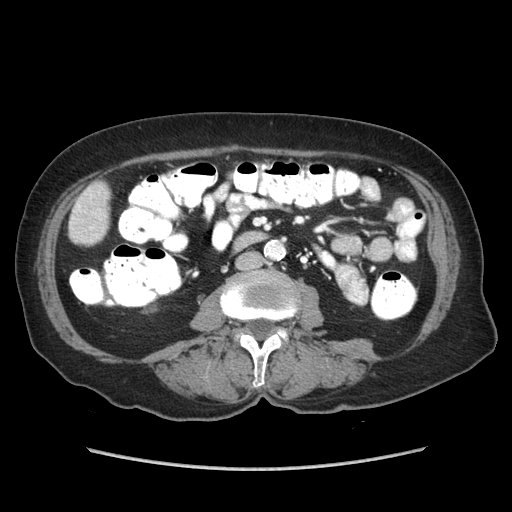
Contrast-enhanced abdominal CT (liver protocol), one axial slice; reconstruction kernel STANDARD; soft-tissue window (W 400 / L 40 HU); 2.5 mm slice thickness; 512 × 512 image matrix, field of view 360 × 360 mm. From the clinical record (not read from this slice): diagnosis: hepatocellular carcinoma (patient treated with transarterial chemoembolisation; whether this scan precedes or follows treatment is not stated here); TNM stage (as recorded): Stage-IIIA; Child-Pugh class: A; tumour differentiation: well differentiated; tumour nodularity: multinodular.
Outlined on this slice (semi-automatically segmented with operator editing):
- liver parenchyma outside the tumour (the mass and vessels are separate outlines, so this box may not span the whole liver): bounding box [x1, y1, x2, y2] px = [70, 182, 108, 244]